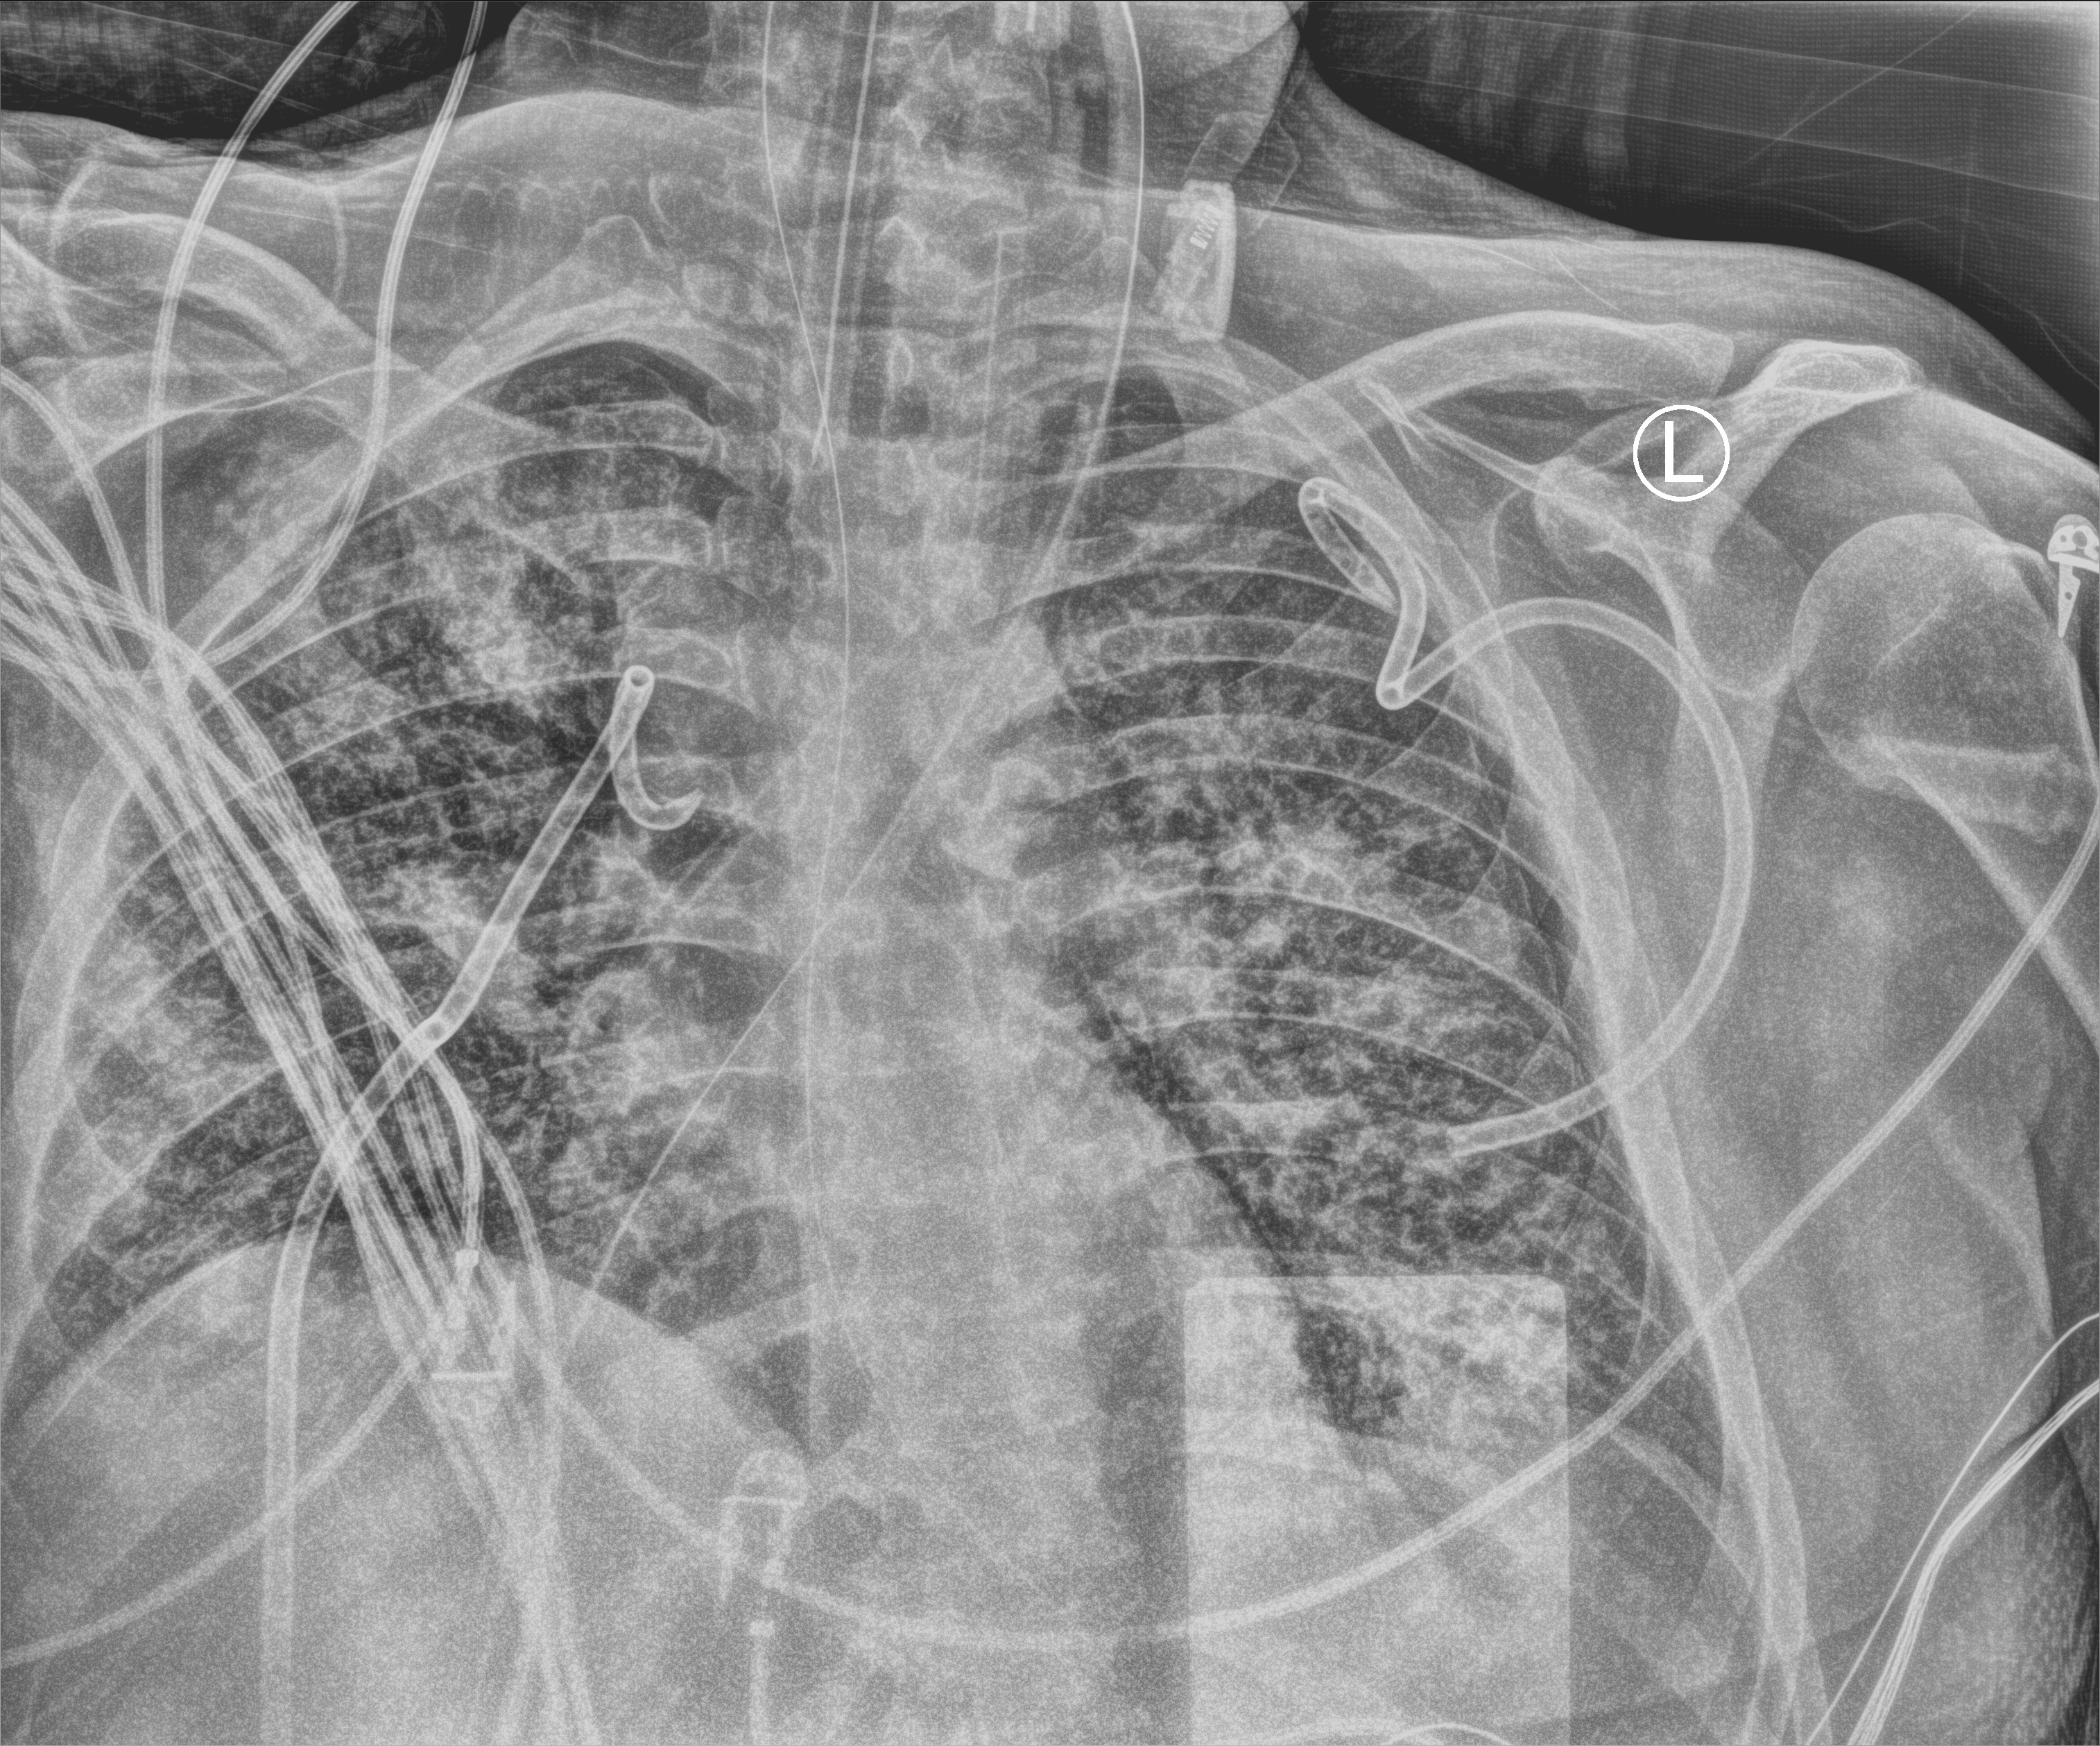
Bedside chest radiograph (computed radiography); anteroposterior (AP) projection. Adult patient hospitalised with COVID-19, age 18–59 years.
From the hospital-stay record, not from the radiograph (when in the stay this image was taken is not recorded): admitted to intensive care during this hospital stay: yes.